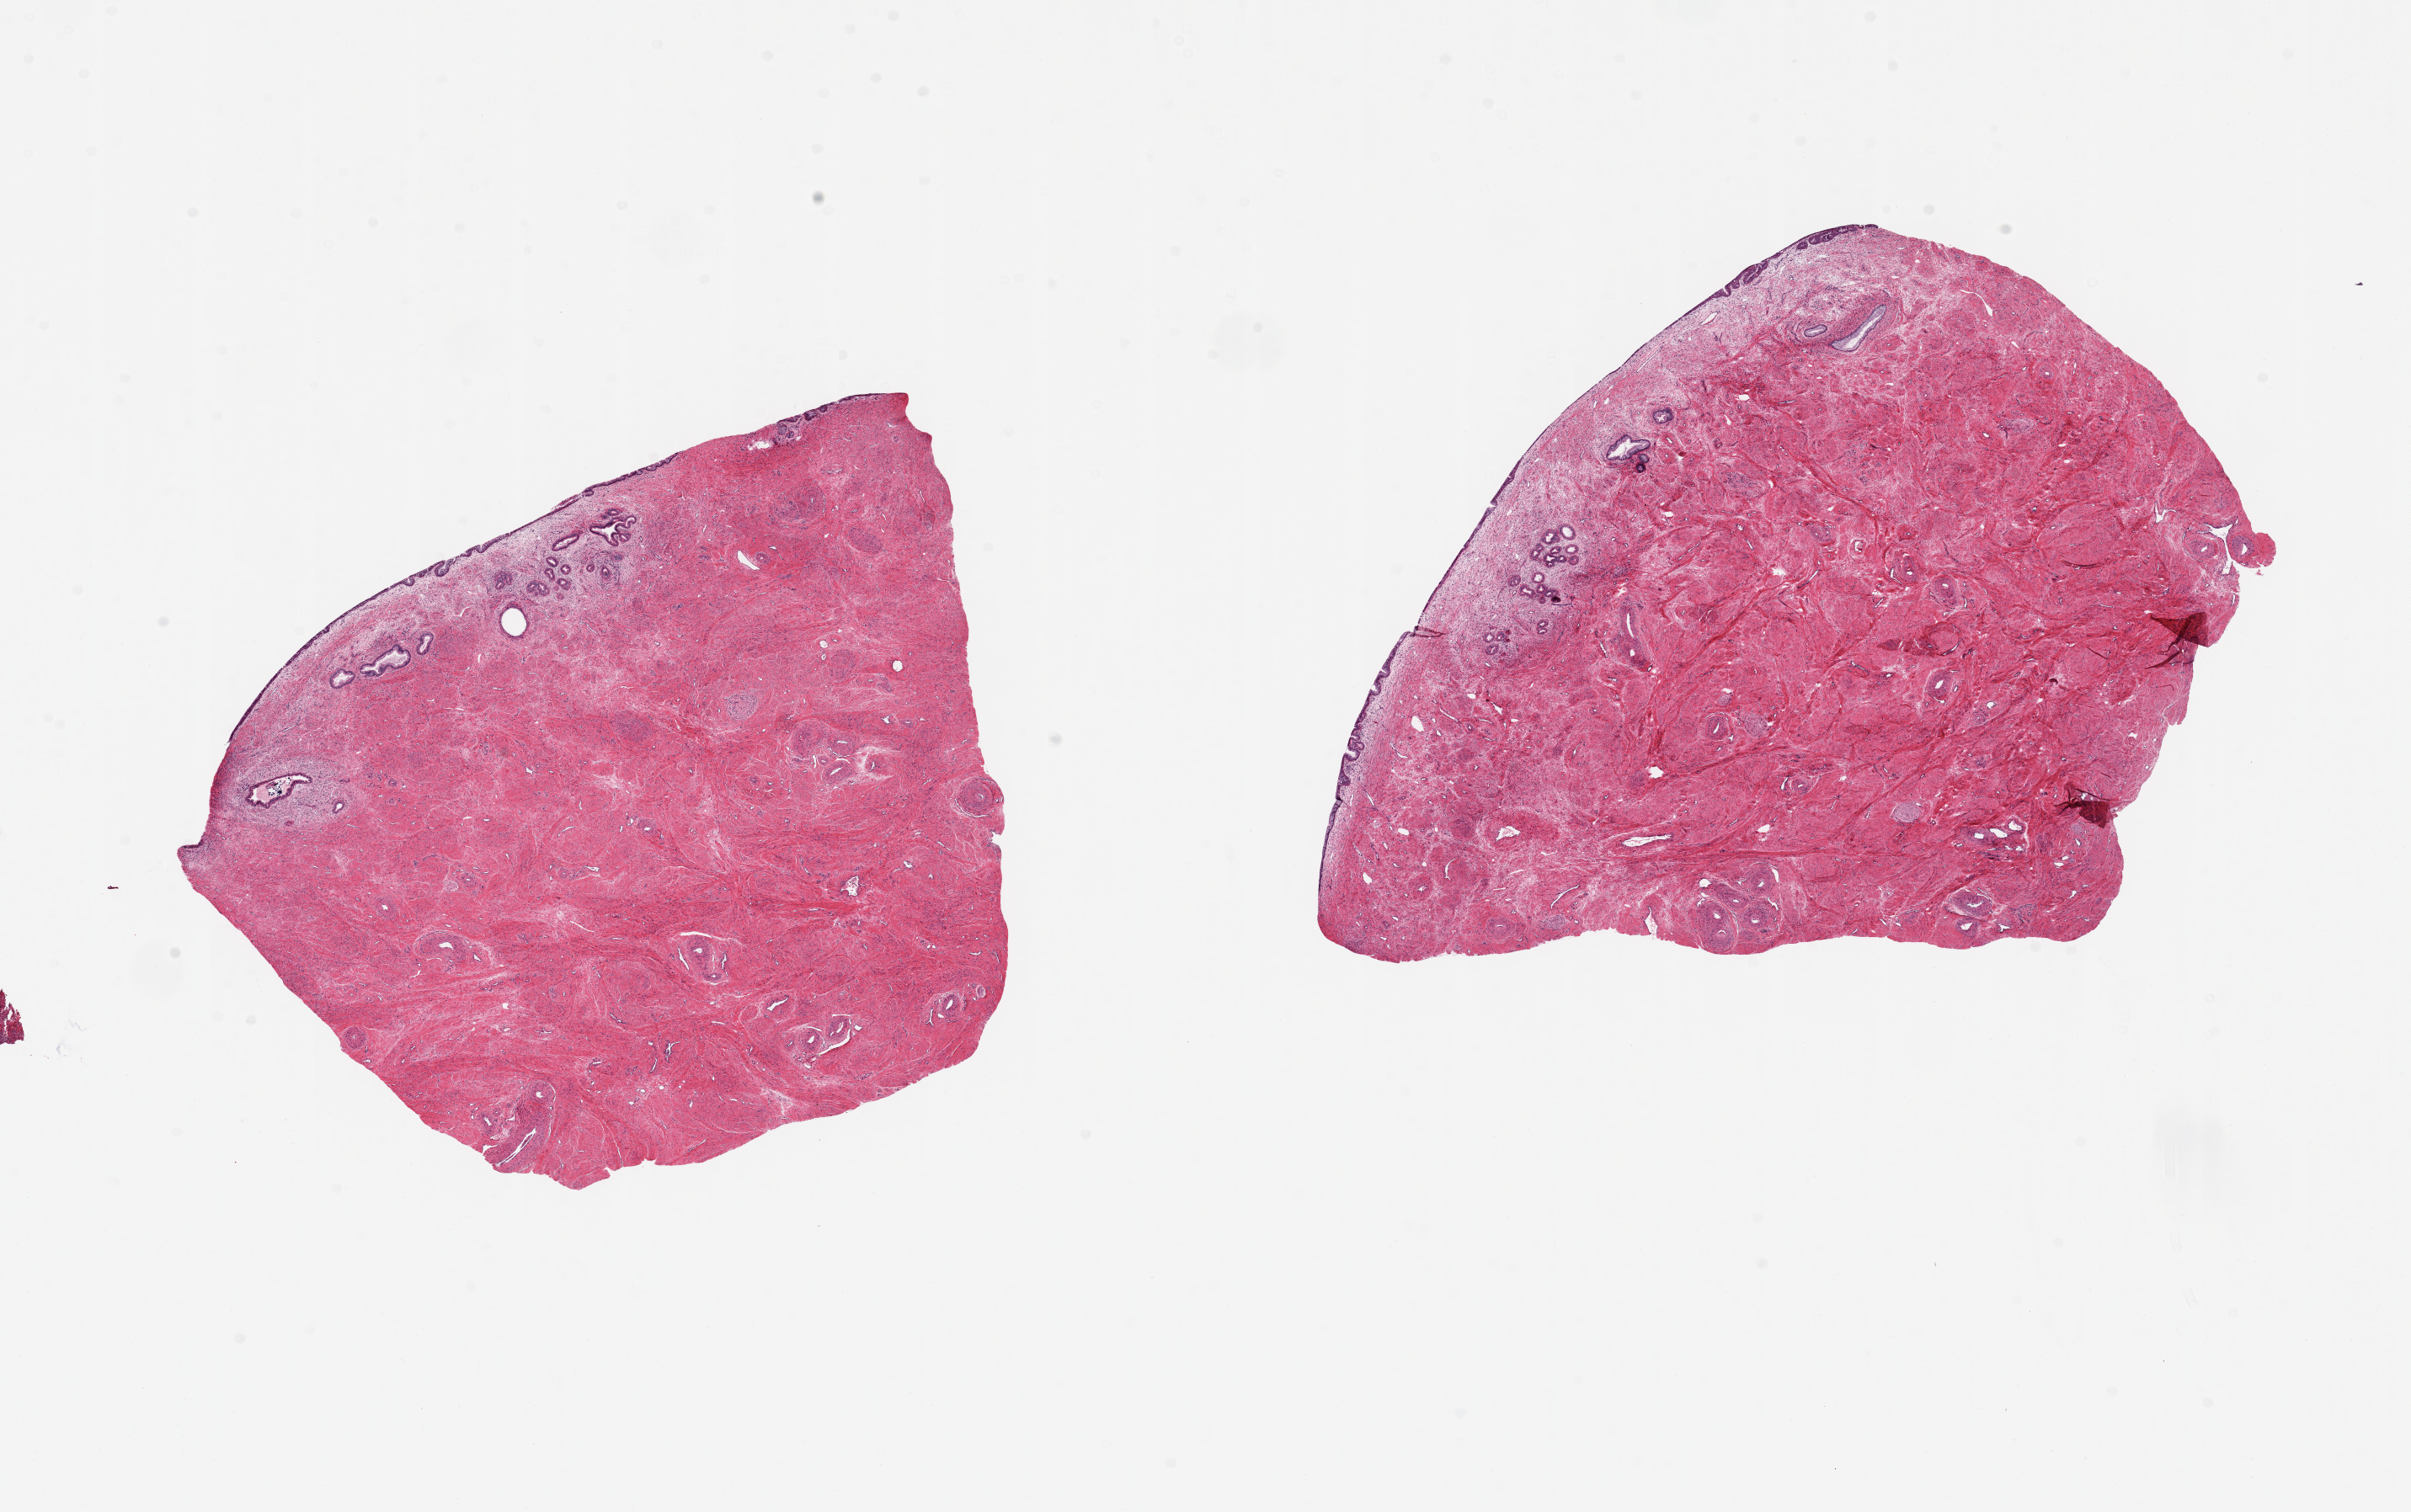
Digitized haematoxylin and eosin-stained section — whole scanned area (about 22.6 x 14.2 mm) shown as a low-resolution overview, PAXgene-fixed, paraffin-embedded tissue, section of endocervix (target tissue), donor tissue sample. Donor: female.
Review note (as recorded): 2 pieces 9x7 & 8x6 mm; good glands and surface epithelium.